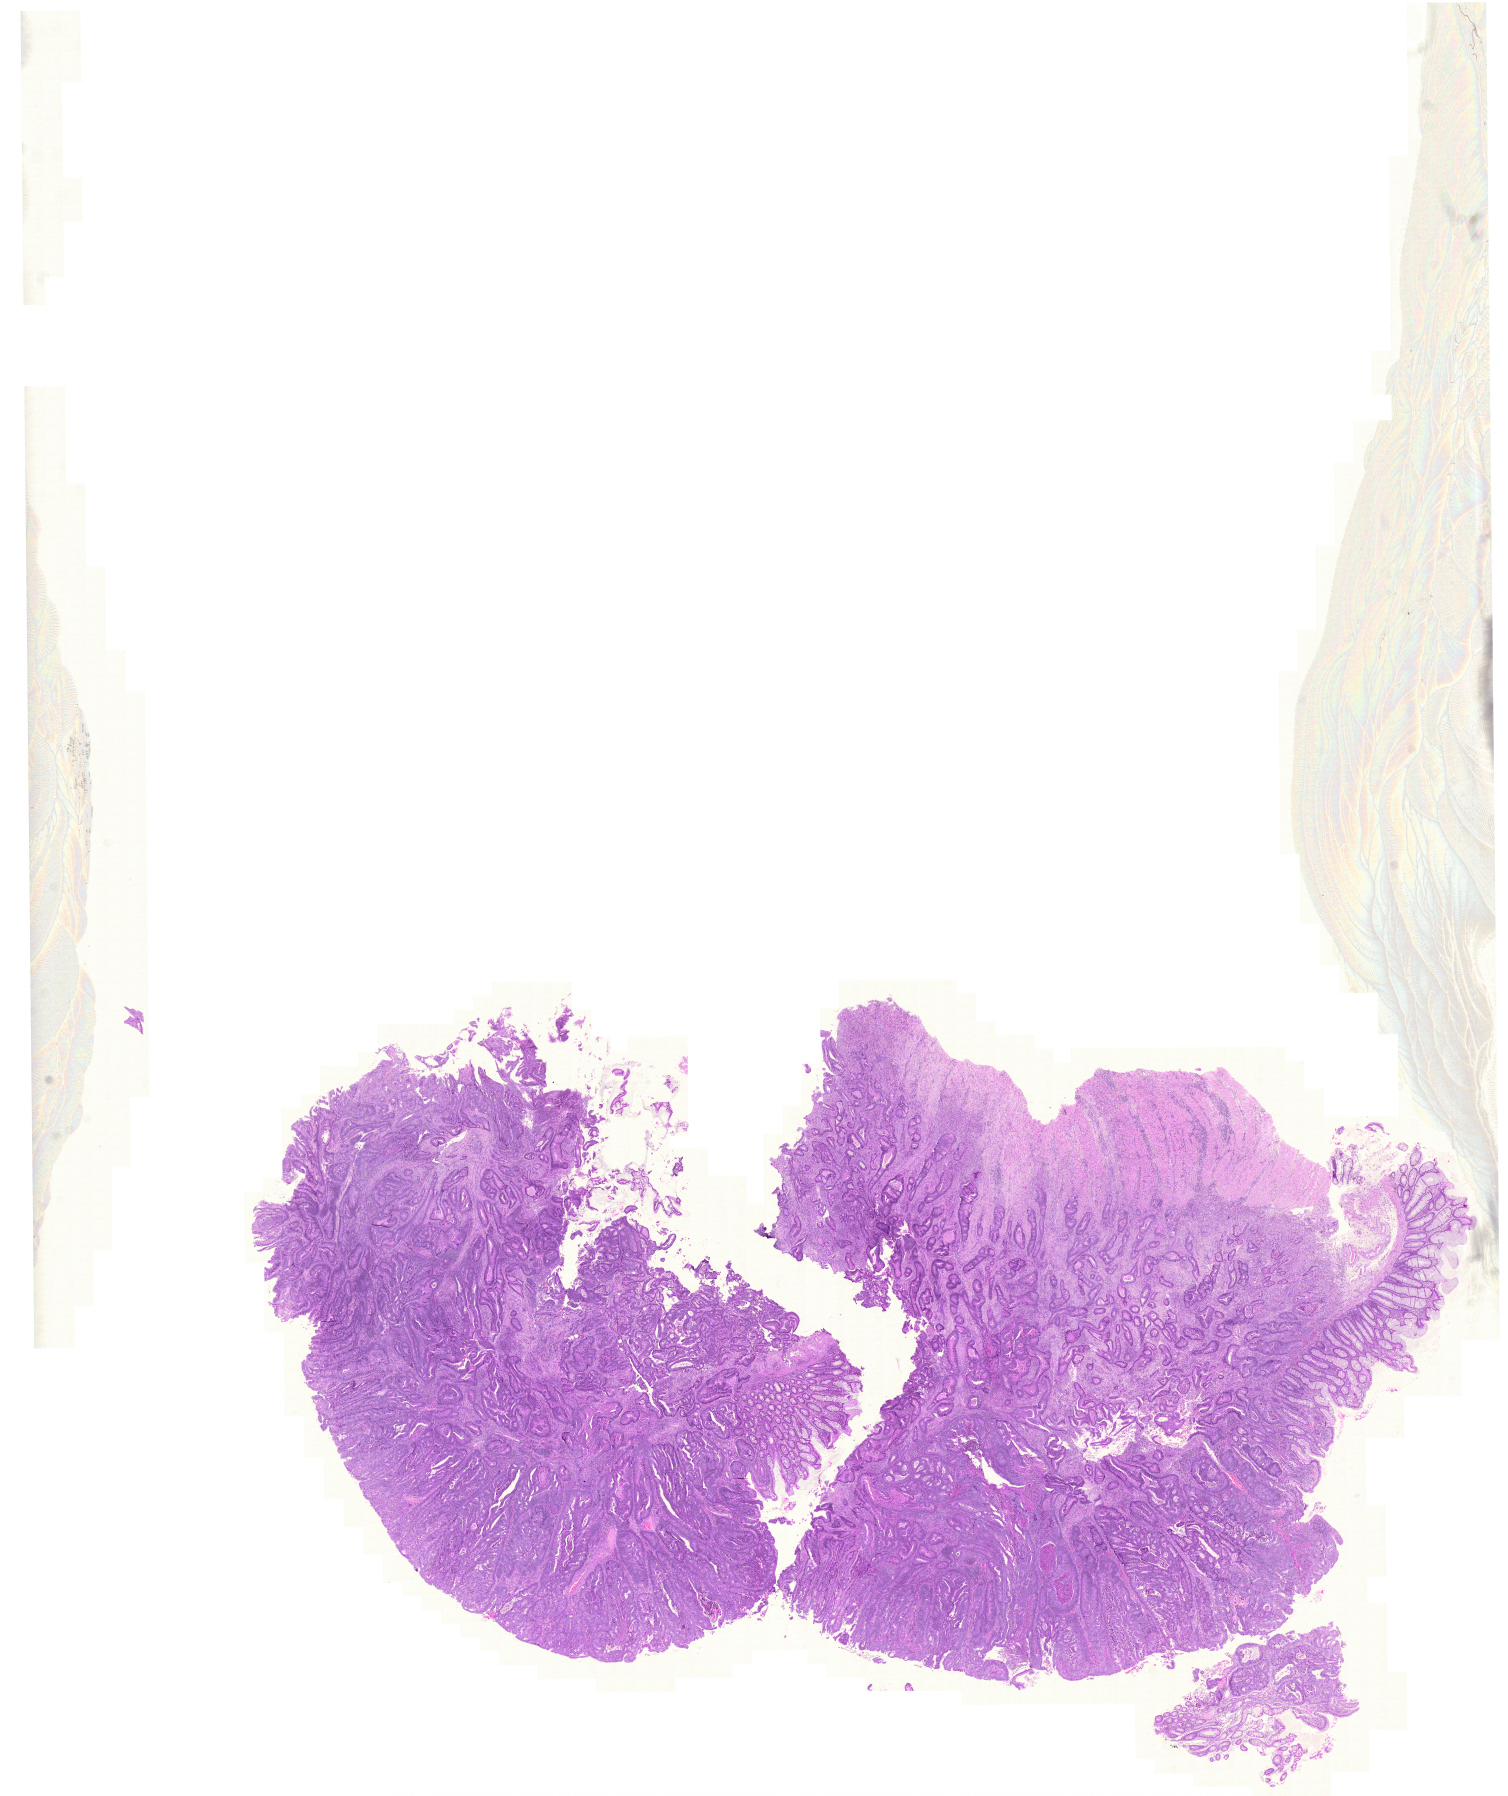
Digitized H&E tissue section (whole slide) — shown as a low-resolution overview of the whole scanned area (about 22.4 x 26.7 mm); formalin-fixed paraffin-embedded (FFPE) diagnostic section; colon, primary tumour sample. Patient: female, age at initial diagnosis 65 years.
* TNM: T2 N0 M0
* histologic diagnosis: Adenocarcinoma, NOS (sigmoid colon)
* lymph nodes positive (case pathology): 0 of 34 examined
* AJCC pathologic stage: I (5th edition)